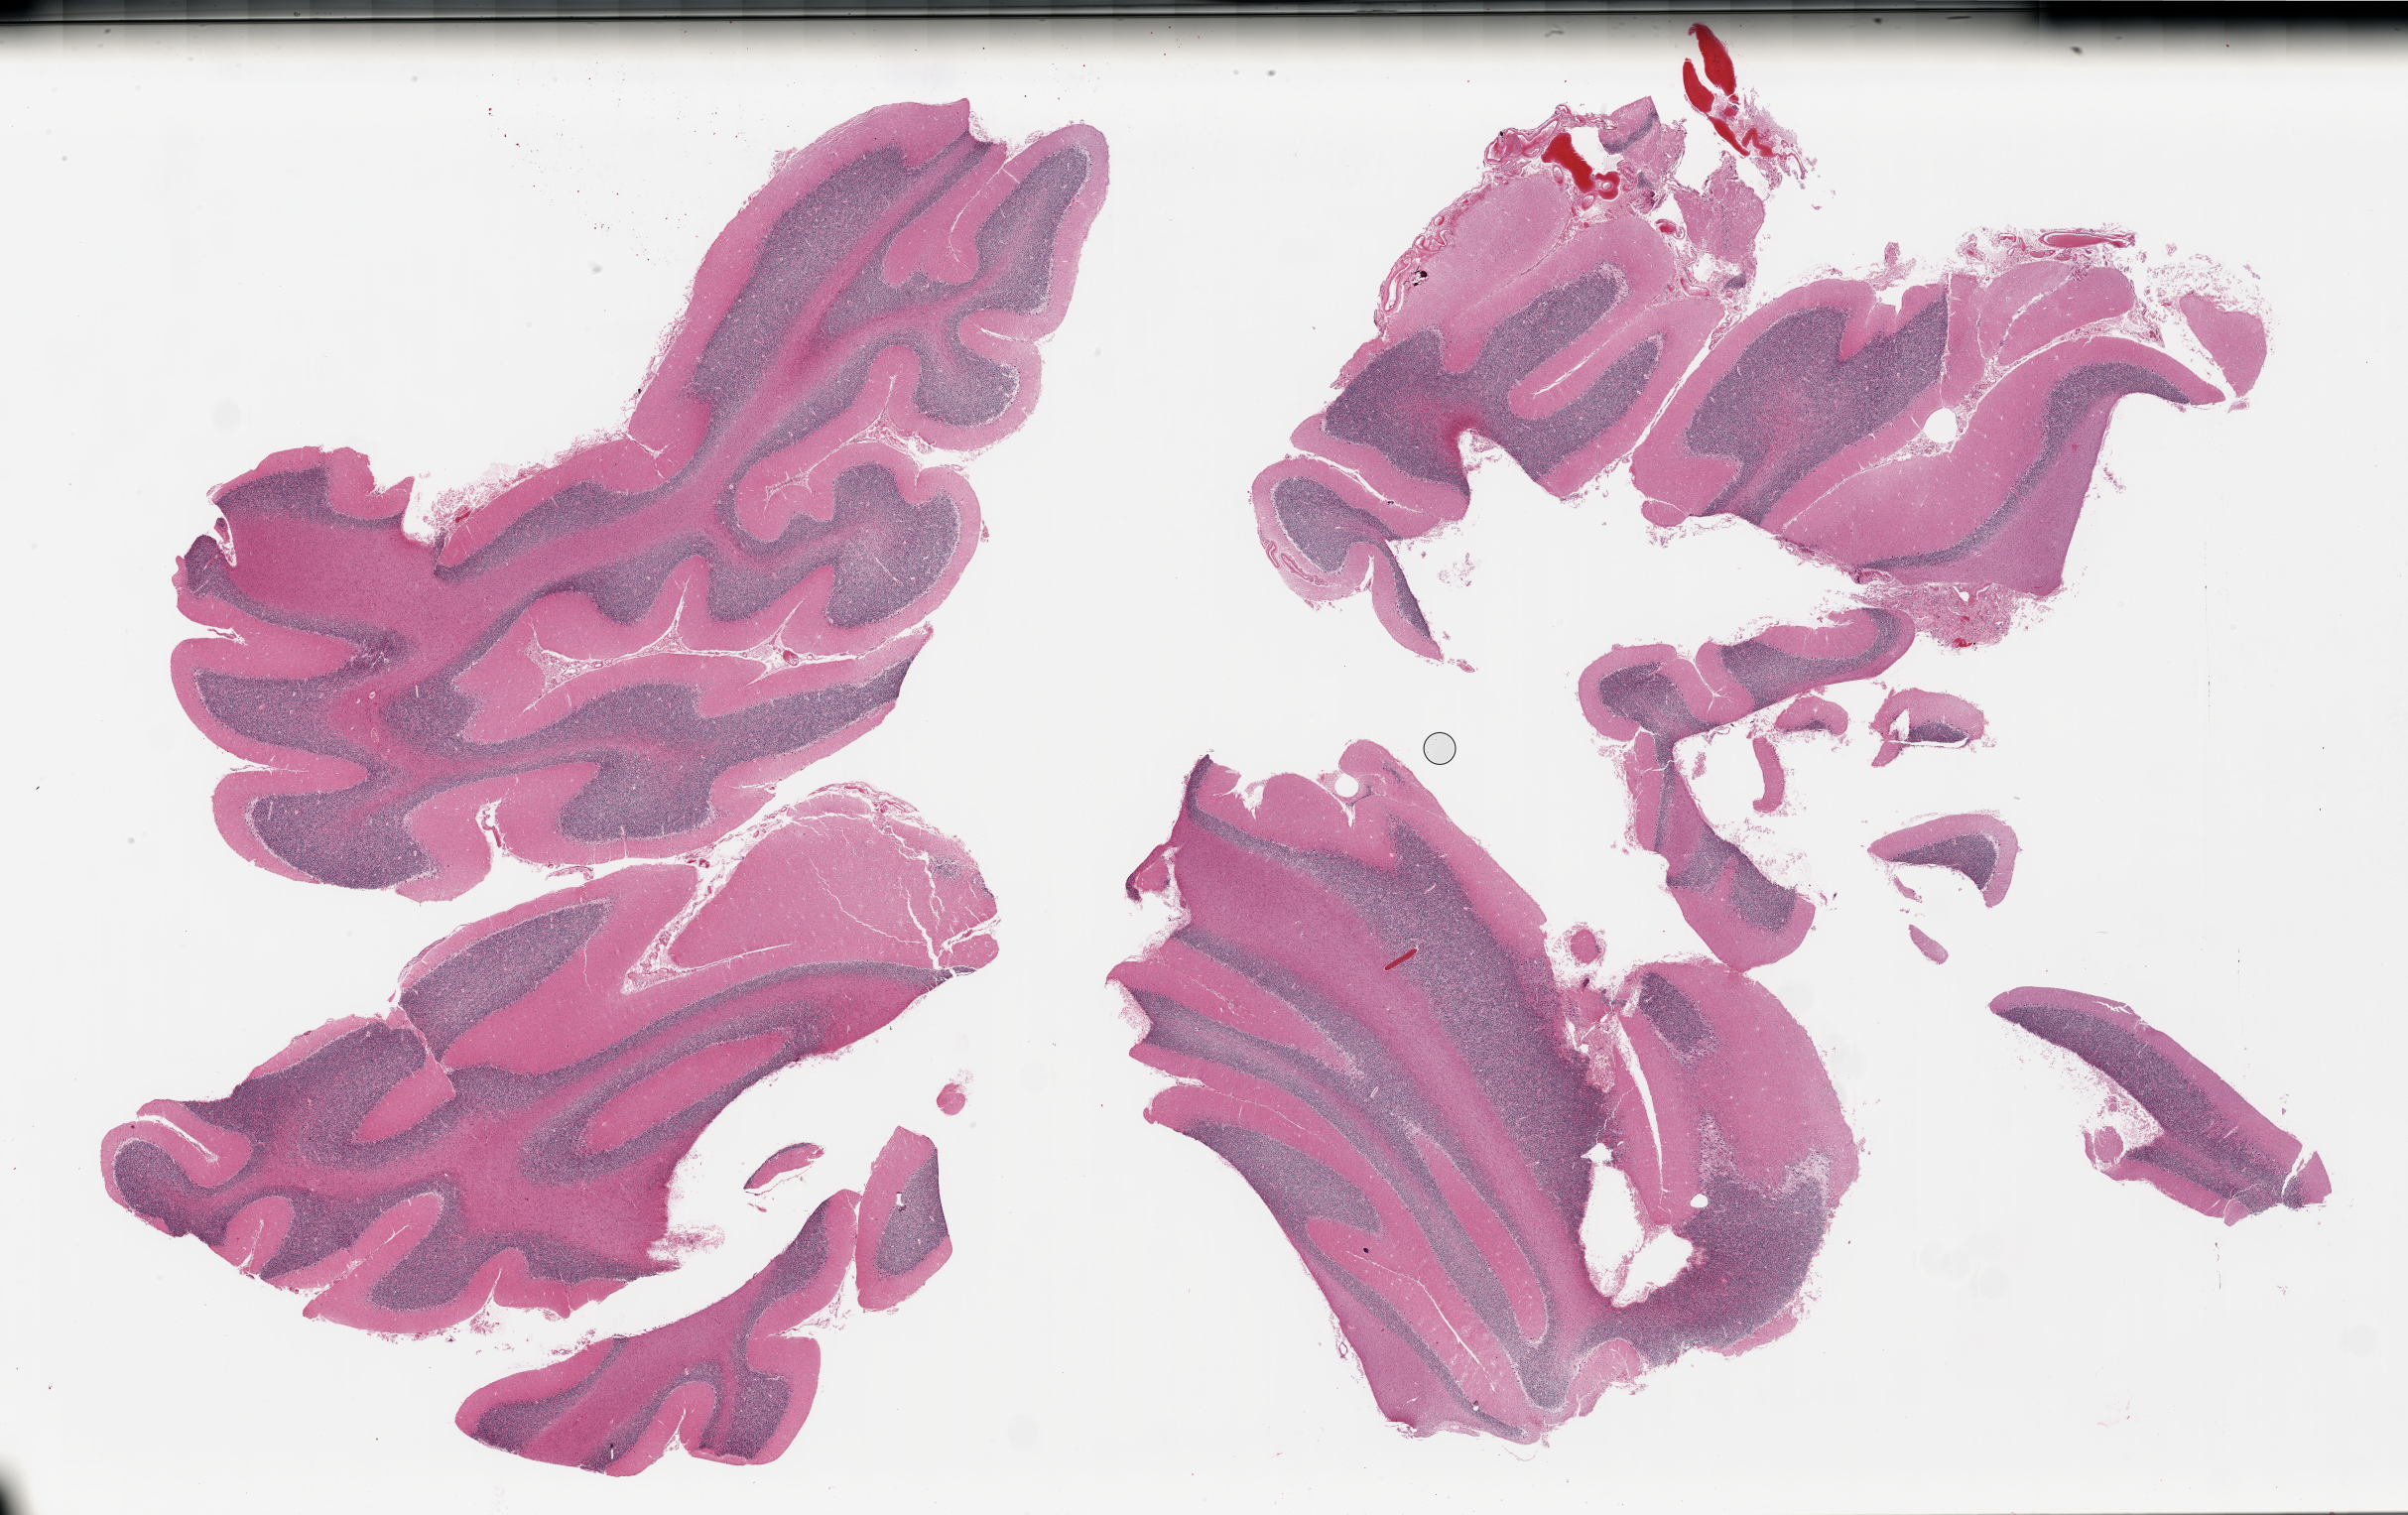
Digitized hematoxylin and eosin (H&E)-stained section — low-resolution overview of the scanned area, about 38.4 x 24.2 mm (from a 20x scan). PAXgene-fixed, paraffin-embedded tissue. Sampled site (target tissue): cerebellum. Donor tissue sample. Male donor.
Pathologist's review note for this sample: 4 fragmented pieces.